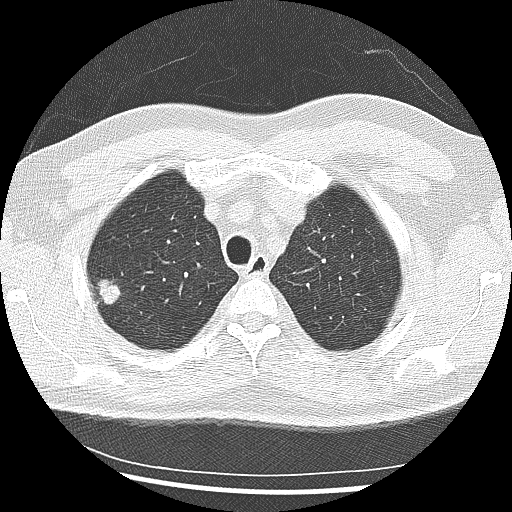
Low-dose screening chest CT, one axial slice. Position 216 of 265 along the scan axis. 120 kVp. Lung window (W 1500 / L -600 HU). 512 × 512 image matrix, field of view 340 × 340 mm.
Annotated regions visible in this slice (expert manual segmentation):
- lesion 1 (tumor, upper lobe of right lung): box from (x=97, y=279) to (x=121, y=305) px